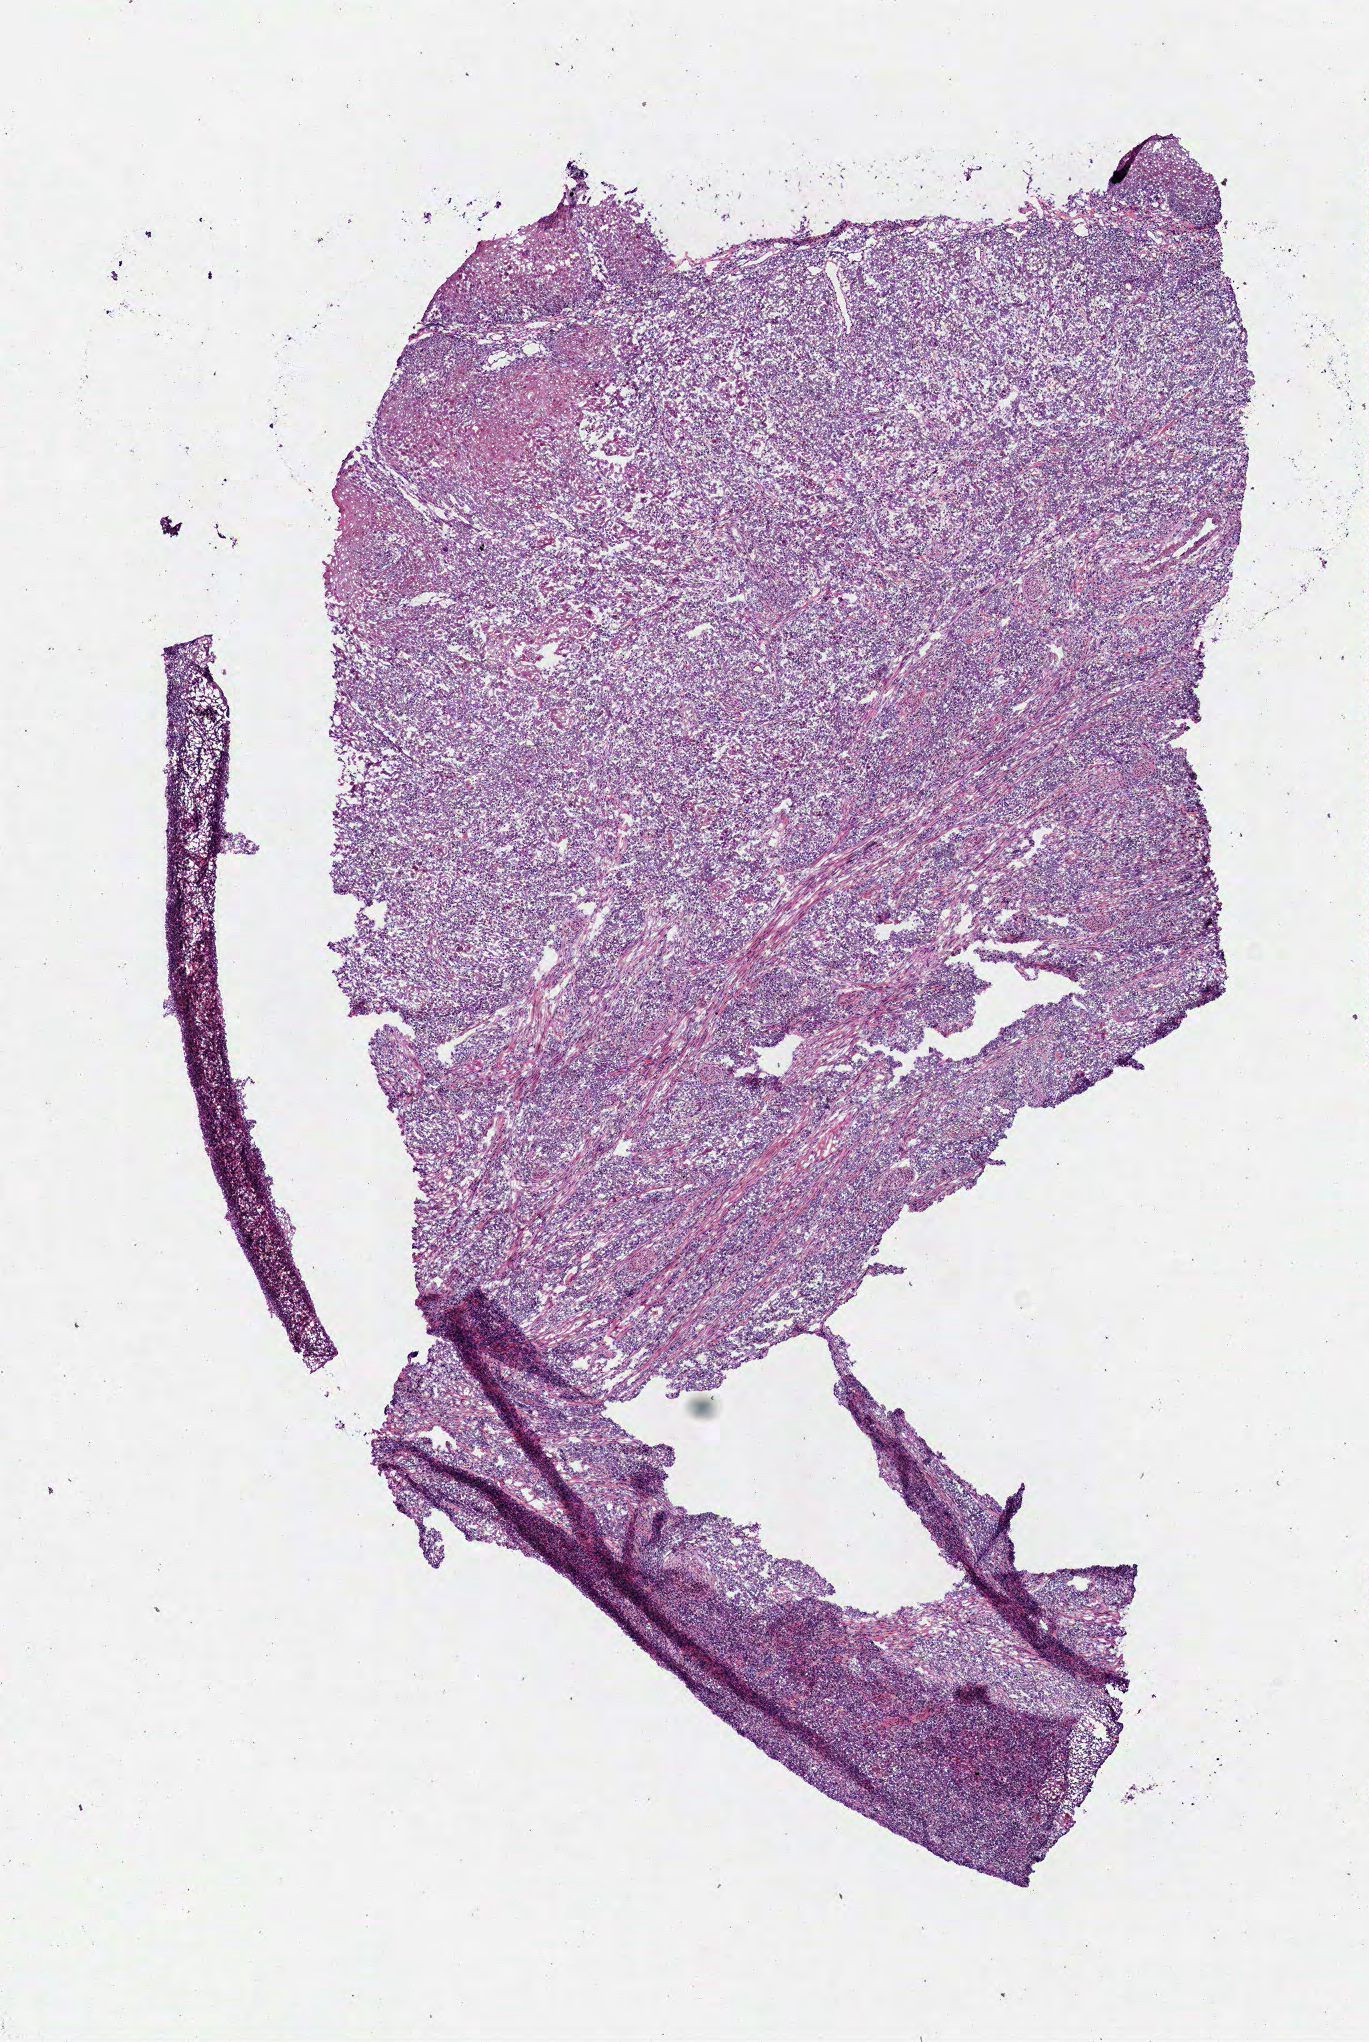
Whole-slide histology image, H&E — low-resolution overview of the scanned area, about 5.4 x 8.0 mm (from a 40x scan); frozen section; primary tumour sample from the head and neck. Female, age 82 years at initial diagnosis. Histologic grade: G3 (poorly differentiated). Slide review estimates, as recorded: tumour cells 90%, tumour nuclei 65%, normal cells 0%, stromal cells 10%, necrosis 0%.
Pathologic diagnosis: Squamous cell carcinoma, NOS (tongue, NOS). AJCC pathologic stage: II (7th edition).